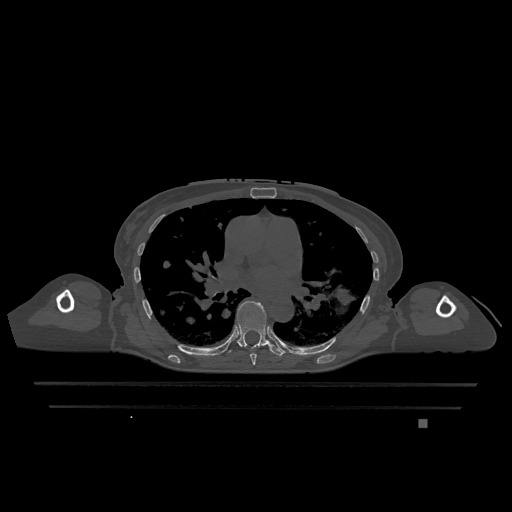
CT including the spine, one axial slice; slice 757 of 1317 in the series (ordered by position); bone window (W 1800 / L 400 HU); 0.5 mm slice thickness; 512 × 512 image matrix, field of view 500 × 500 mm. Female patient, age 74 years. Case-level facts recorded for this patient, not image findings: primary cancer: lung; vertebrae with lytic lesions (as recorded): T1, T4, T5, T6, L4, L5.
Annotated regions visible in this slice (semi-automatic segmentation, software-assisted and operator-edited):
- T6 vertebra: bounding box (x1, y1, x2, y2) in pixels: (250, 353, 257, 365)
- T7 vertebra: (223, 301, 285, 356)